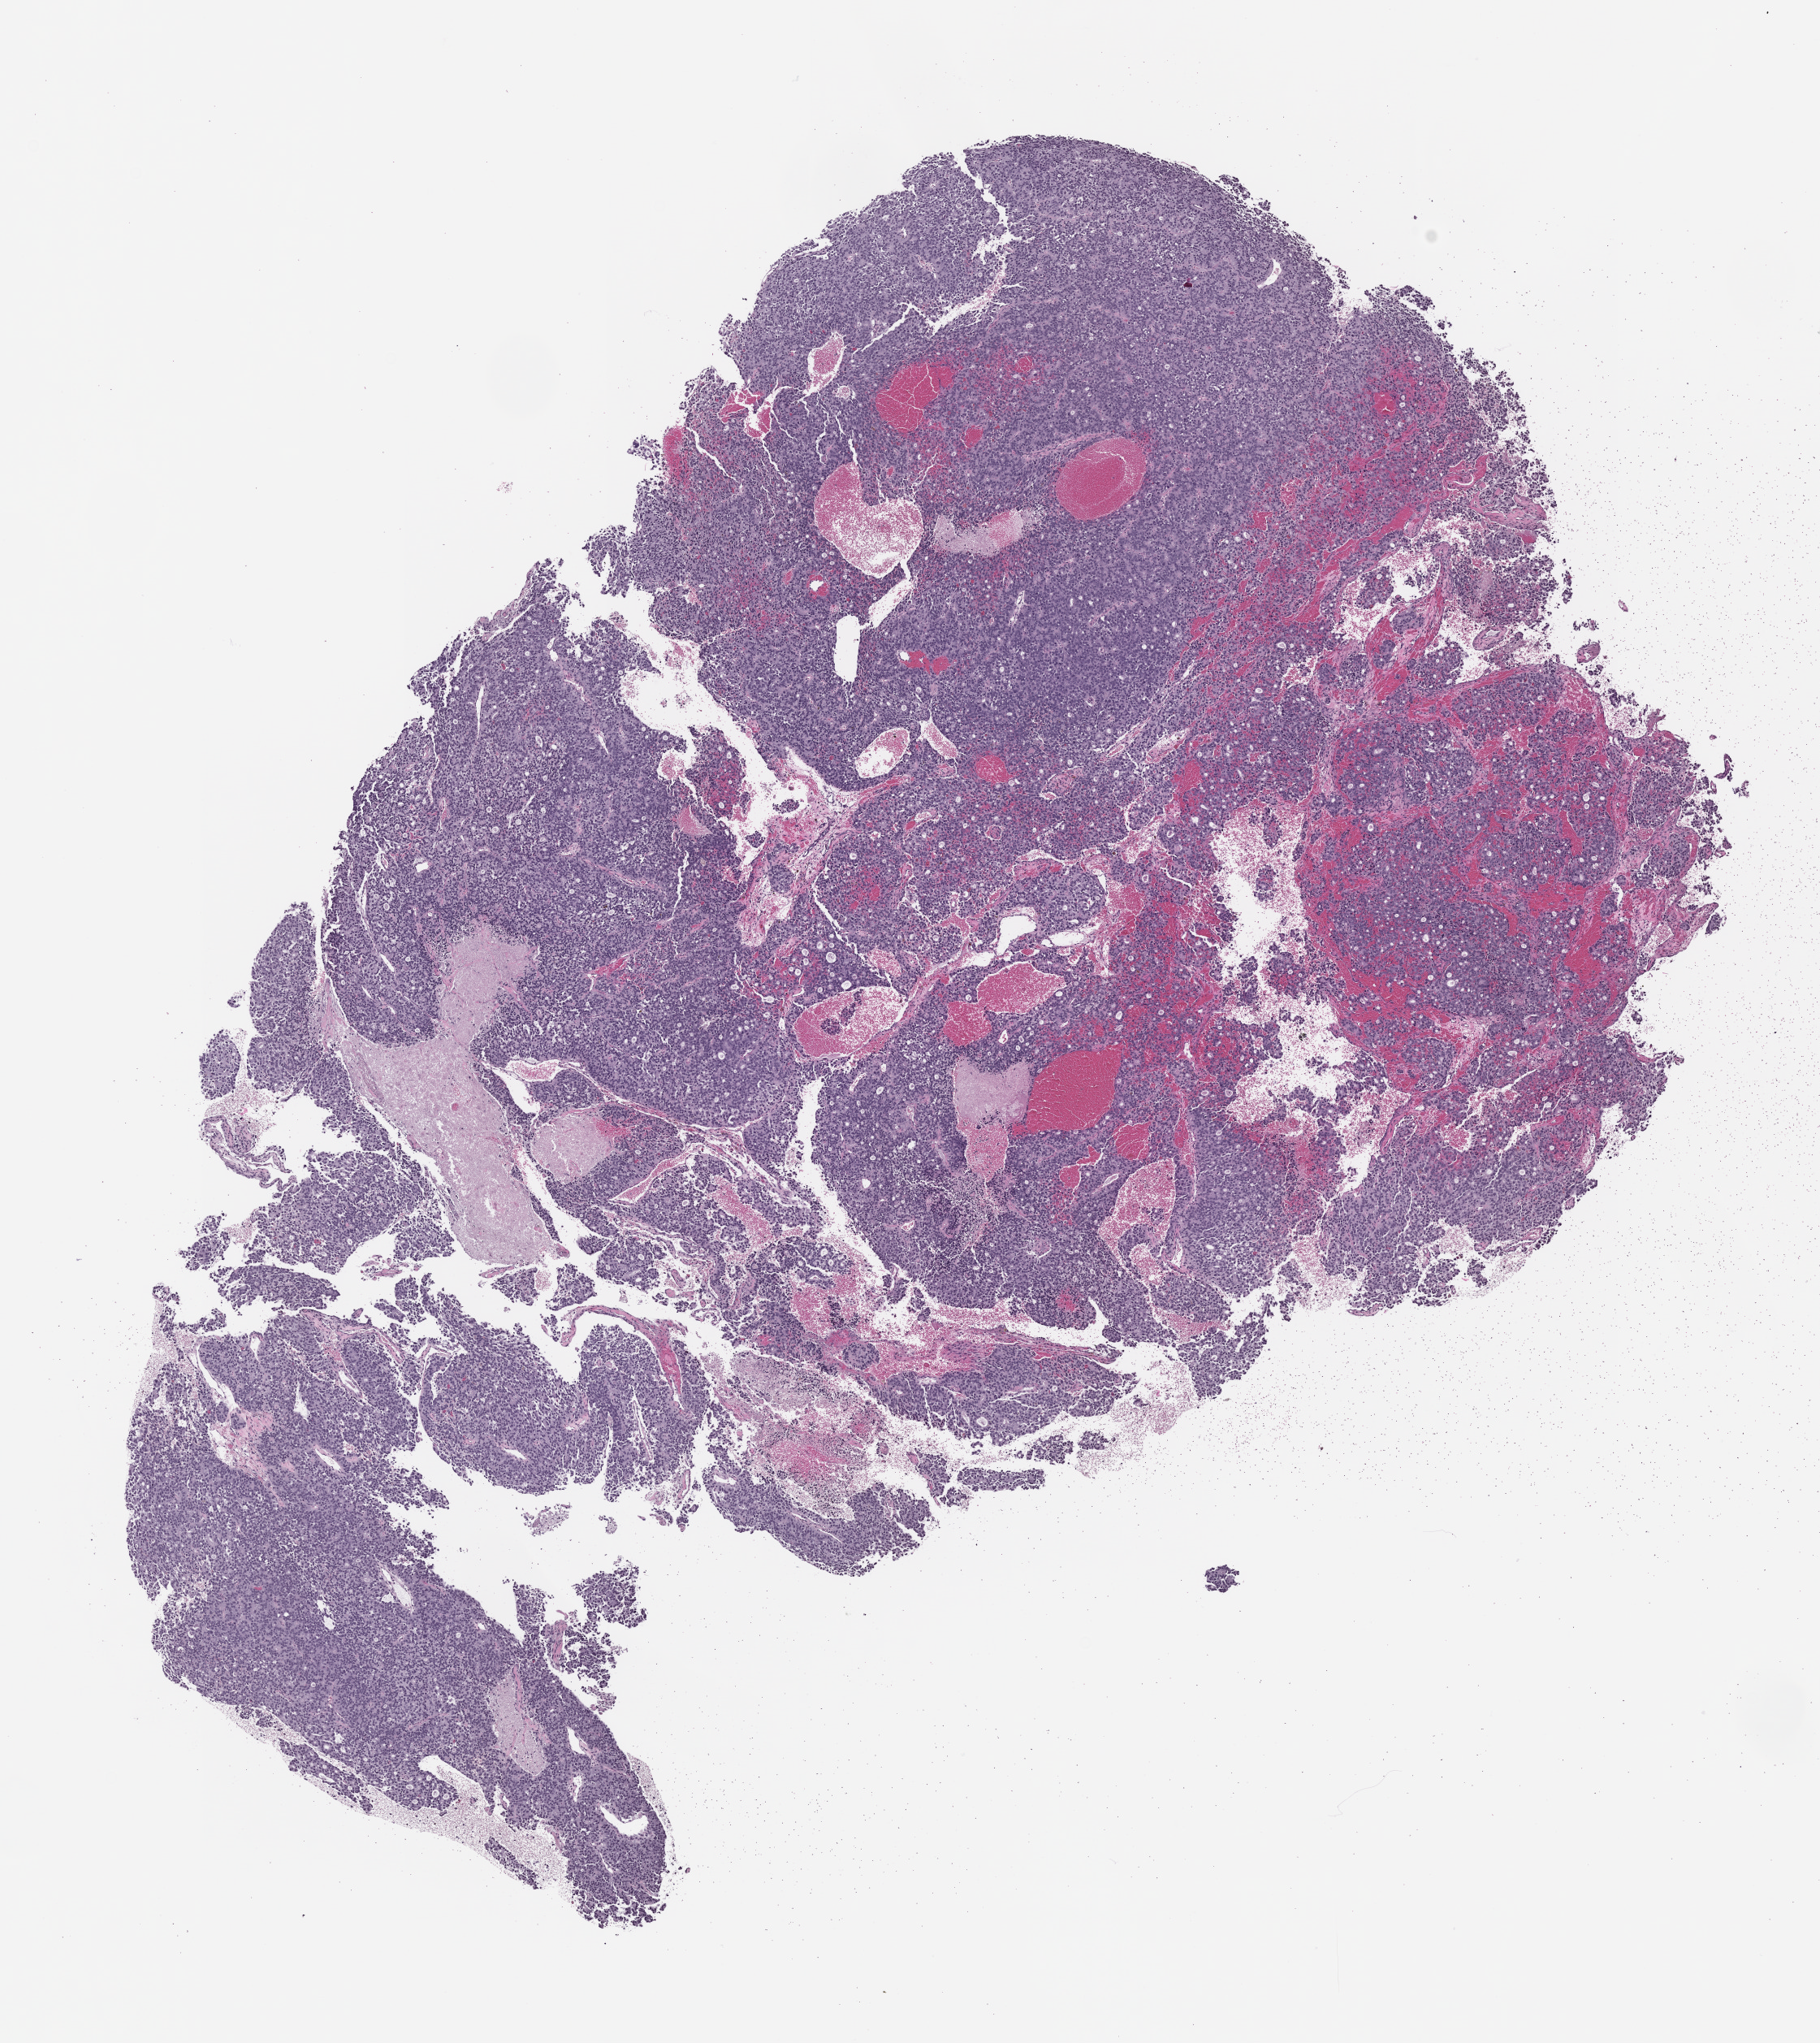
H&E whole-slide image of a patient-derived xenograft (PDX) tumor grown in a mouse, whole scanned area (about 9.0 x 10.1 mm) shown as a low-resolution overview; FFPE section; tumor site category: prostate.
- originating patient diagnosis: Prostate Carcinoma